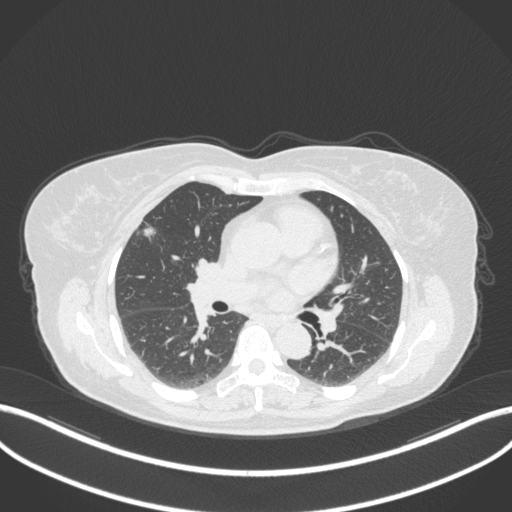
Chest CT, one axial slice; slice 184 of 310 in the series (ordered by position); reconstruction kernel B31f; lung window (W 1500 / L -600 HU); 1 mm slice thickness; 512 × 512 image matrix, field of view 400 × 400 mm. Patient: female, 55 years. Case-level facts recorded for this patient, not image findings: clinical TNM (as recorded): T1b N0 M0; histopathological grade: G2.
Annotated regions visible in this slice (bounding box drawn by a radiologist):
- lung tumour (recorded histology: adenocarcinoma): bounding box <140,218,158,240> (left, top, right, bottom; pixels)